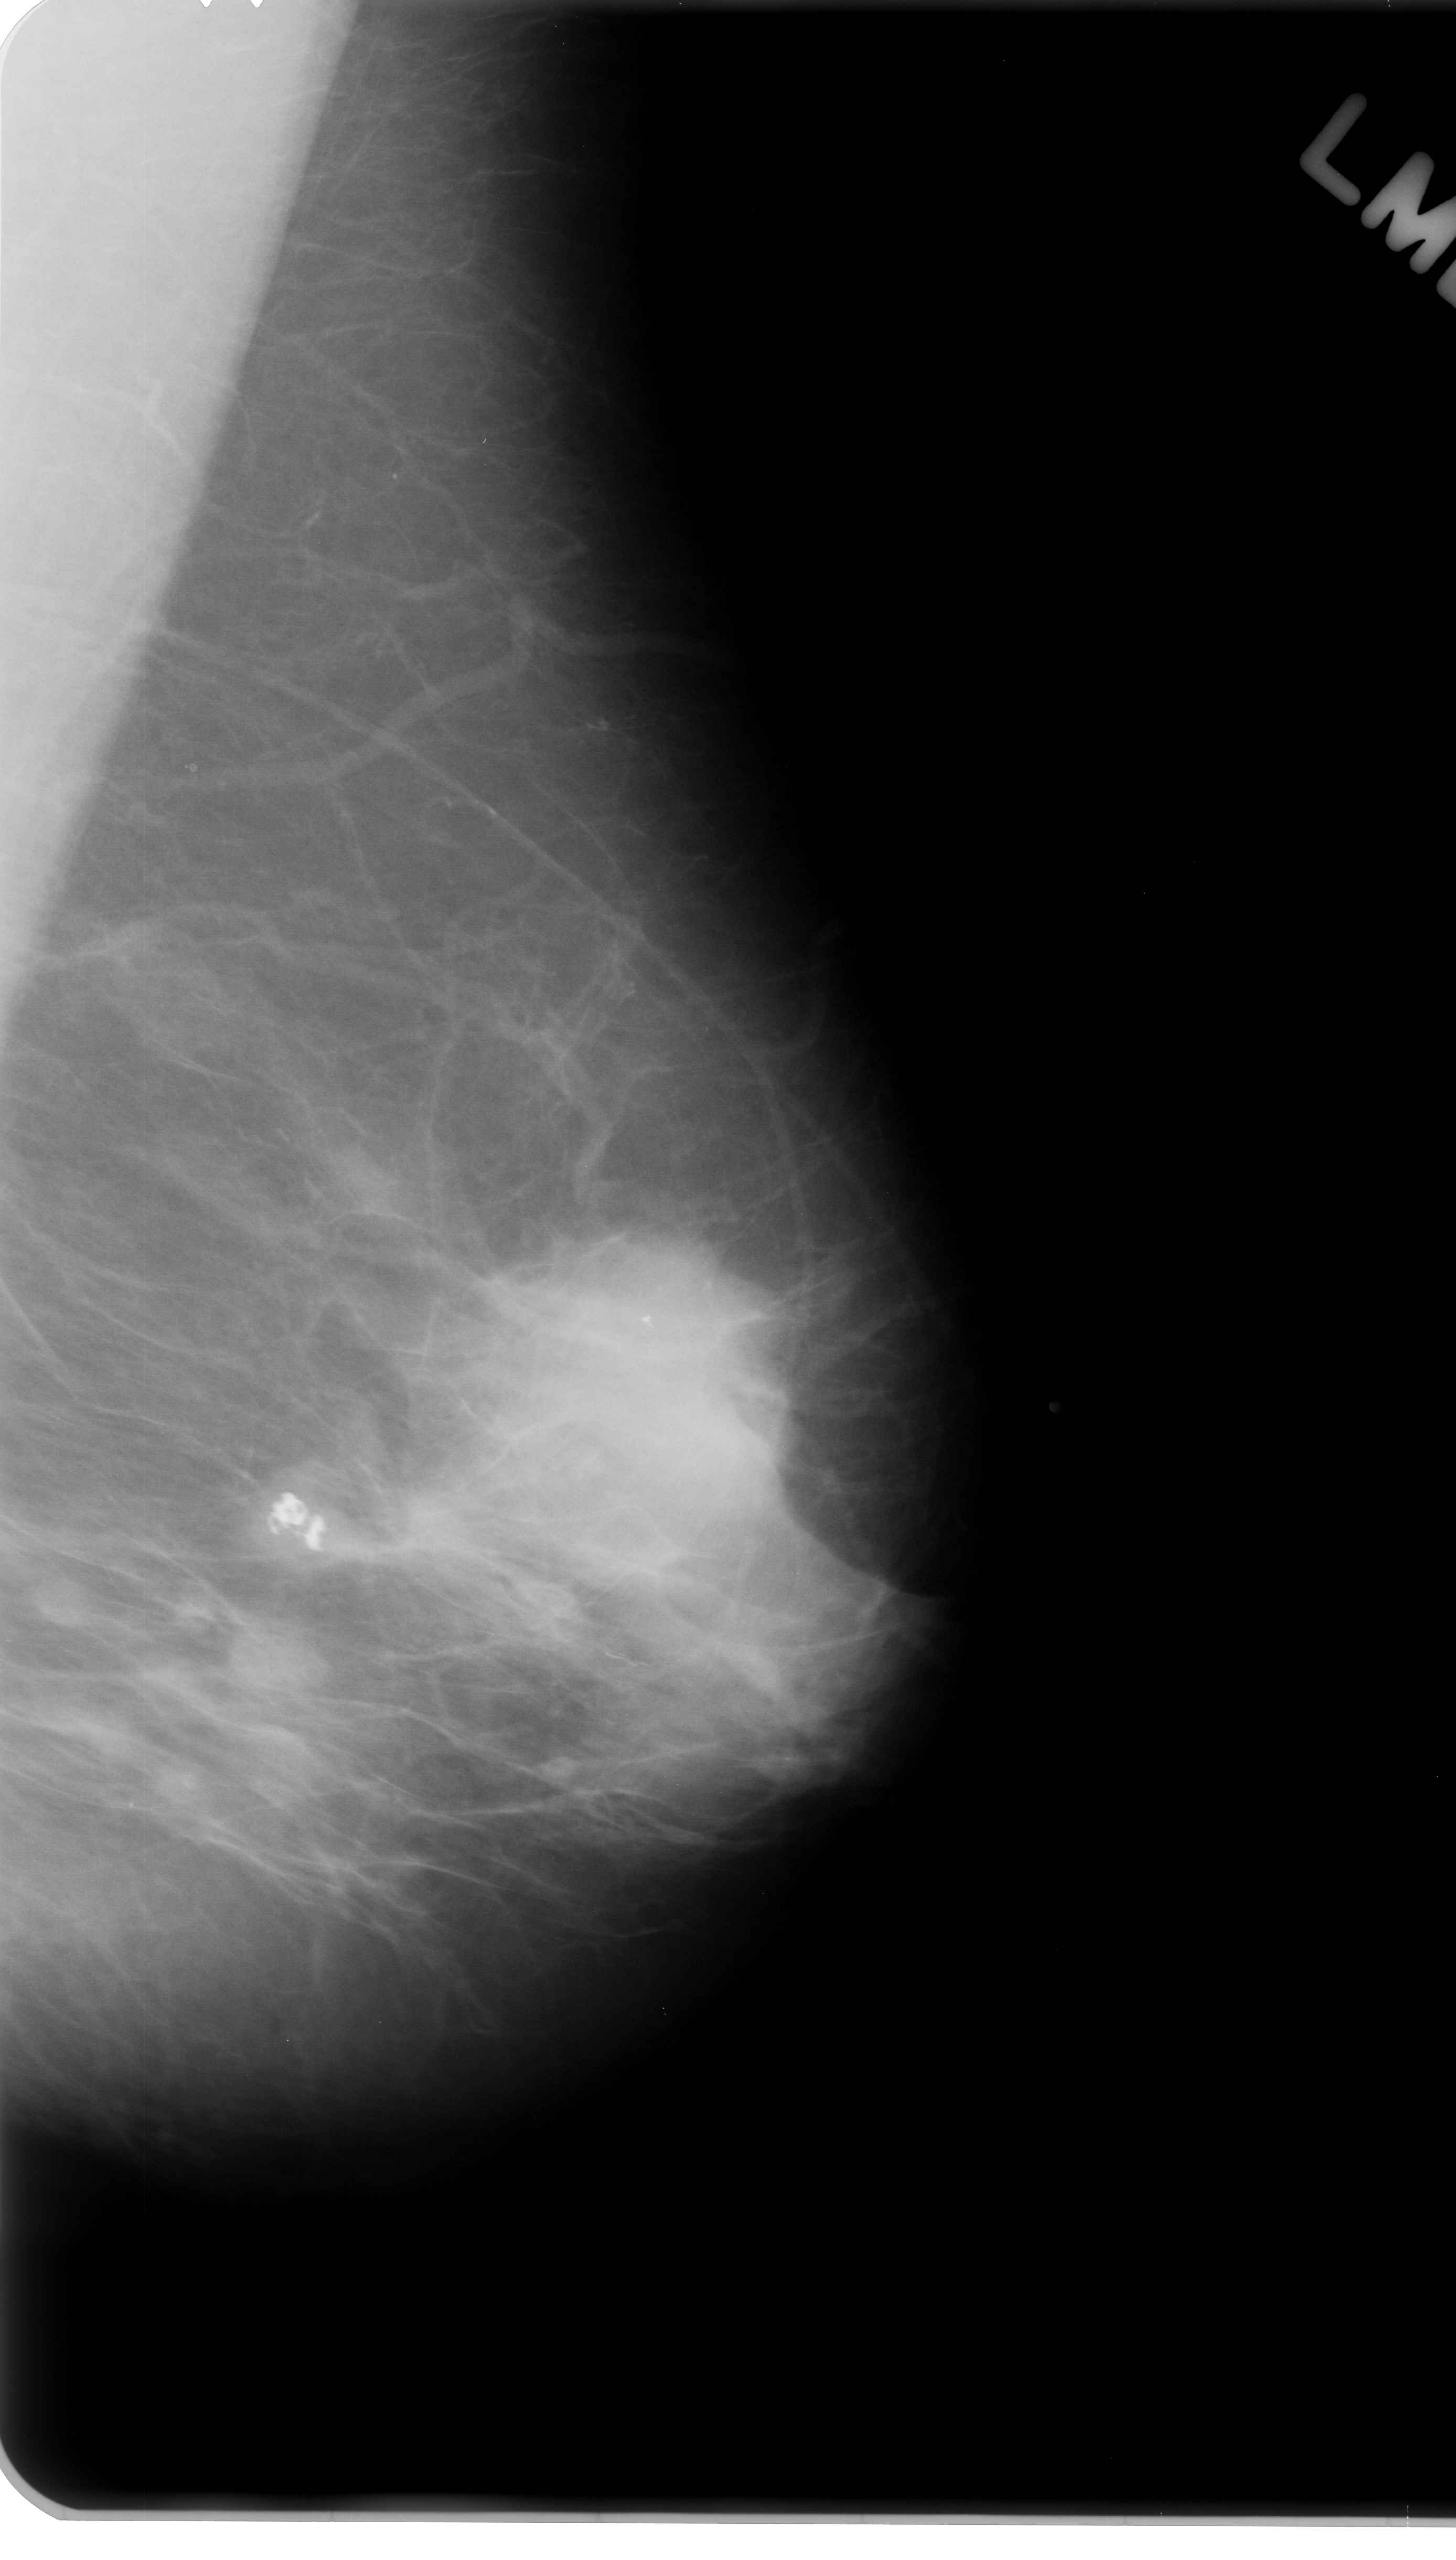
Mammogram (digitized film). Left breast. MLO view. Breast composition: scattered fibroglandular densities (BI-RADS density category 2 of 4). 1456 × 2560 image matrix.
Expert-marked regions of interest on this image (one box per marked abnormality):
- mass, shape round, margins ill defined; BI-RADS assessment category 4; subtlety rating 5 on a 1 (subtle) to 5 (obvious) scale; pathology result (as recorded, not read from the image): malignant: bounding box [x1, y1, x2, y2] px = [509, 1270, 820, 1555]